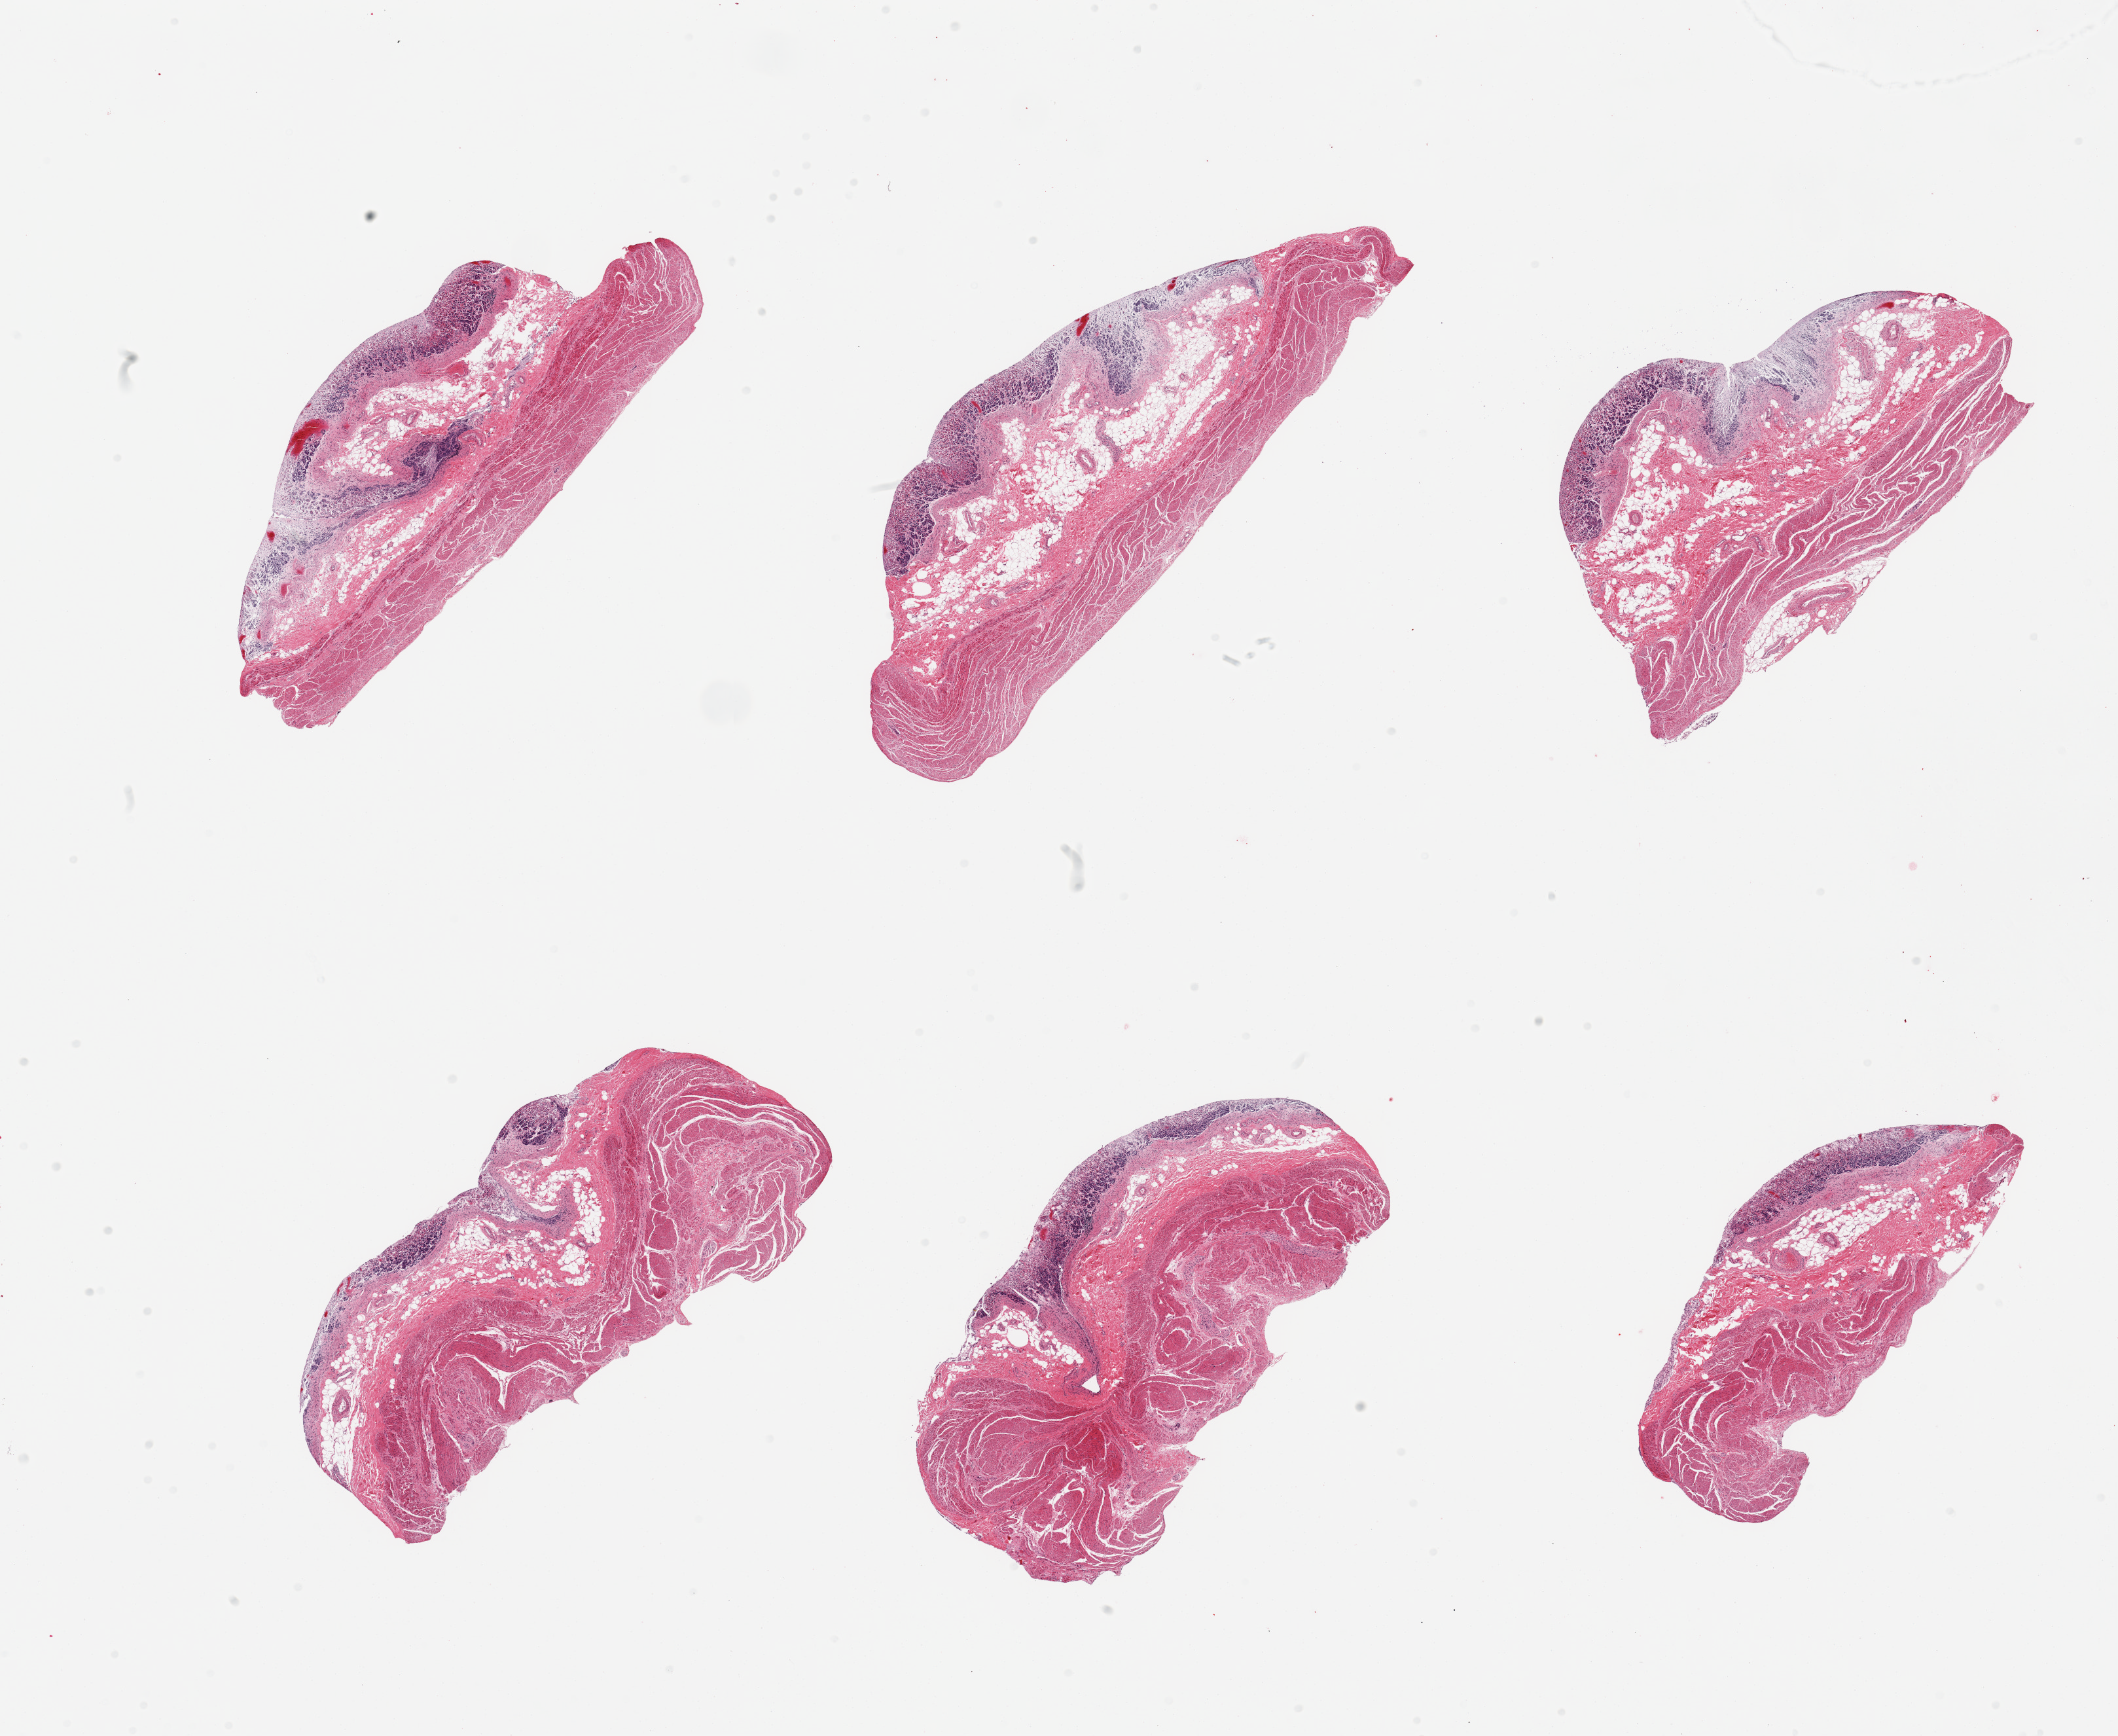
Whole-slide image, haematoxylin and eosin stain, brightfield — low-resolution overview of the scanned area, about 25.6 x 21.0 mm. PAXgene-fixed, paraffin-embedded tissue. Target tissue: stomach. Tissue donor sample.
• review note (as recorded): 6 pieces; autolyzed gastric mucosa grade 2/3 and preserved muscularis